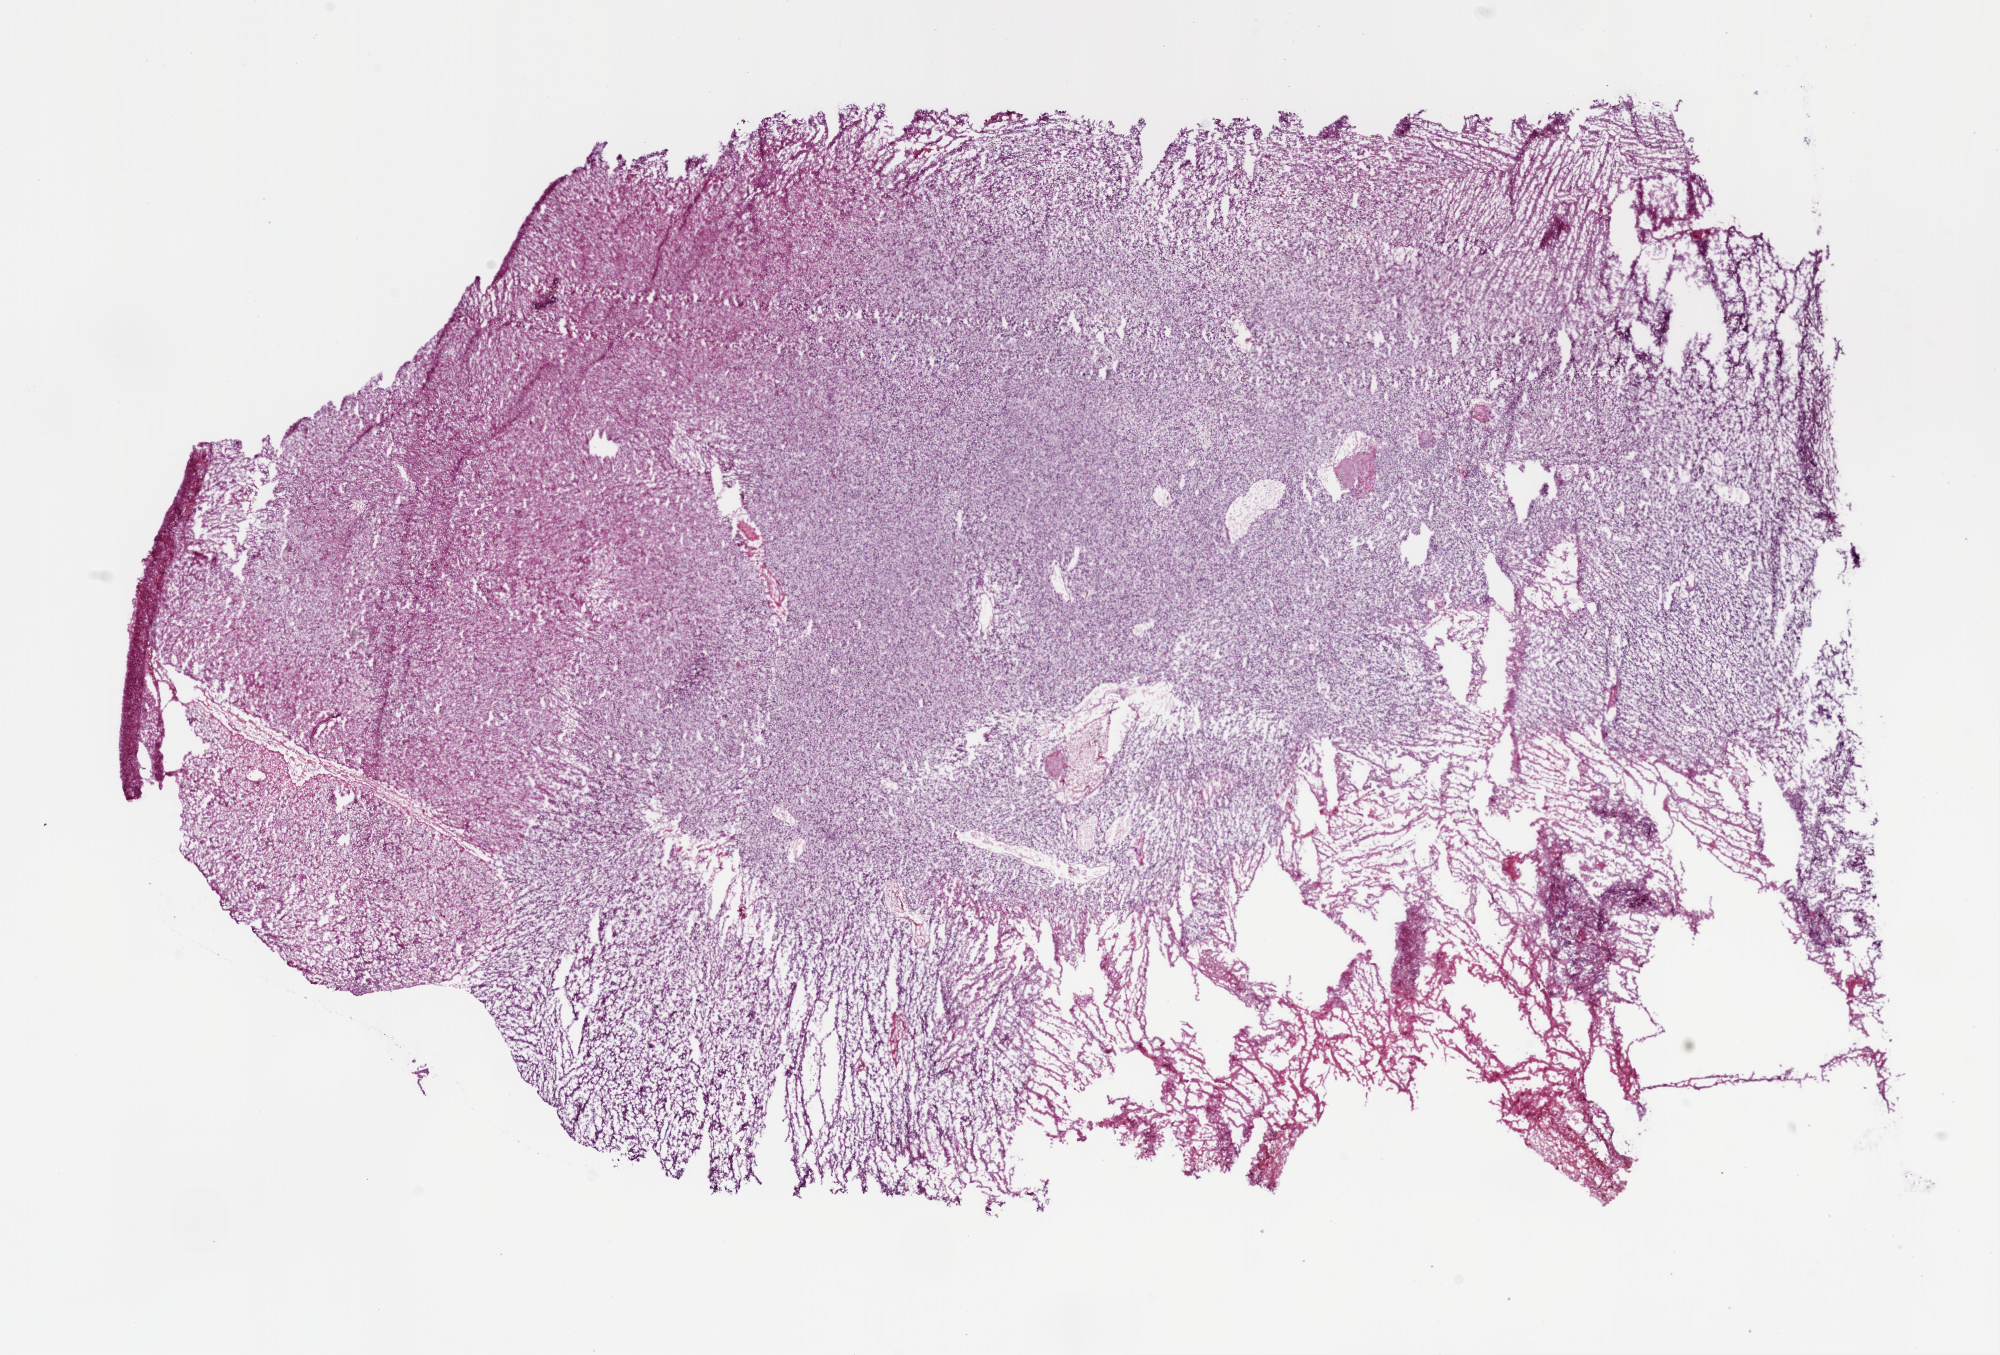
H&E whole-slide image, low-resolution overview of the scanned area, about 16.0 x 10.9 mm, frozen section from the bottom of the tissue portion, primary tumour sample from the brain. Patient: male, age at initial diagnosis 66 years. Pathologist review of this section (percent, as recorded): tumour cells 83%, tumour nuclei 75%, normal cells 0%, stromal cells 0%, necrosis 12%.
• histologic diagnosis: Glioblastoma